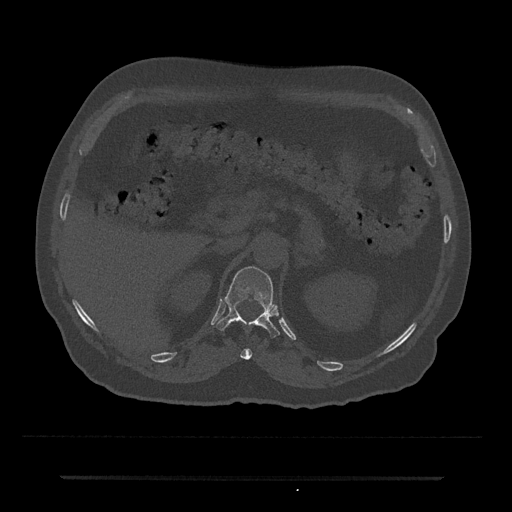
CT including the spine, one axial slice; slice 137 of 797 in the series (ordered by position); reconstruction kernel Br40s/3; 120 kVp; bone window (W 1800 / L 400 HU); 0.5 mm slice thickness; 512 × 512 image matrix, field of view 437 × 437 mm. Male patient, age 69 years. From the clinical record (not read from this slice): primary cancer: prostate.
Annotated regions visible in this slice (semi-automatically segmented with operator editing):
- T11 vertebra: bounding box [x1, y1, x2, y2] px = [234, 320, 252, 360]
- T12 vertebra: [215, 266, 280, 338]